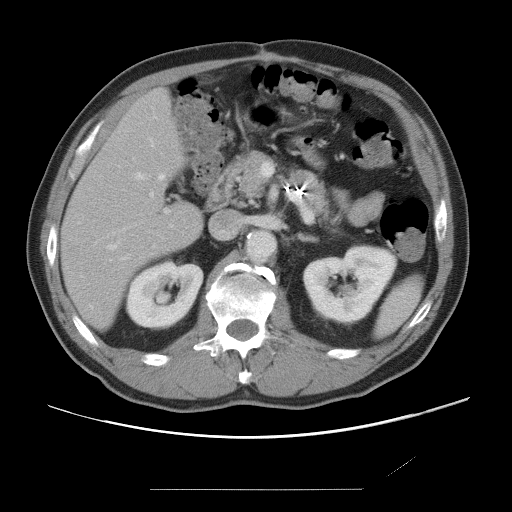
Contrast-enhanced abdominal CT, one axial slice; position 36 of 87 along the scan axis; 120 kVp; intravenous contrast given; soft-tissue window (W 400 / L 40 HU); 5 mm slice thickness; 512 × 512 image matrix, field of view 406 × 406 mm. Male patient, age 74 years. From the clinical record (not read from this slice): diagnosis: colorectal cancer liver metastases, imaged before liver resection; multiple liver metastases: yes; largest metastasis: 1.1 cm.
Outlined on this slice (manually delineated by an expert):
- hepatic veins: box from (x=90, y=140) to (x=164, y=308) px
- liver: (x=64, y=90)–(x=203, y=327)
- planned liver remnant (the part of the liver to remain after resection): (x=64, y=90)–(x=203, y=327)
- portal vein (with intrahepatic branches): (x=150, y=162)–(x=274, y=227)